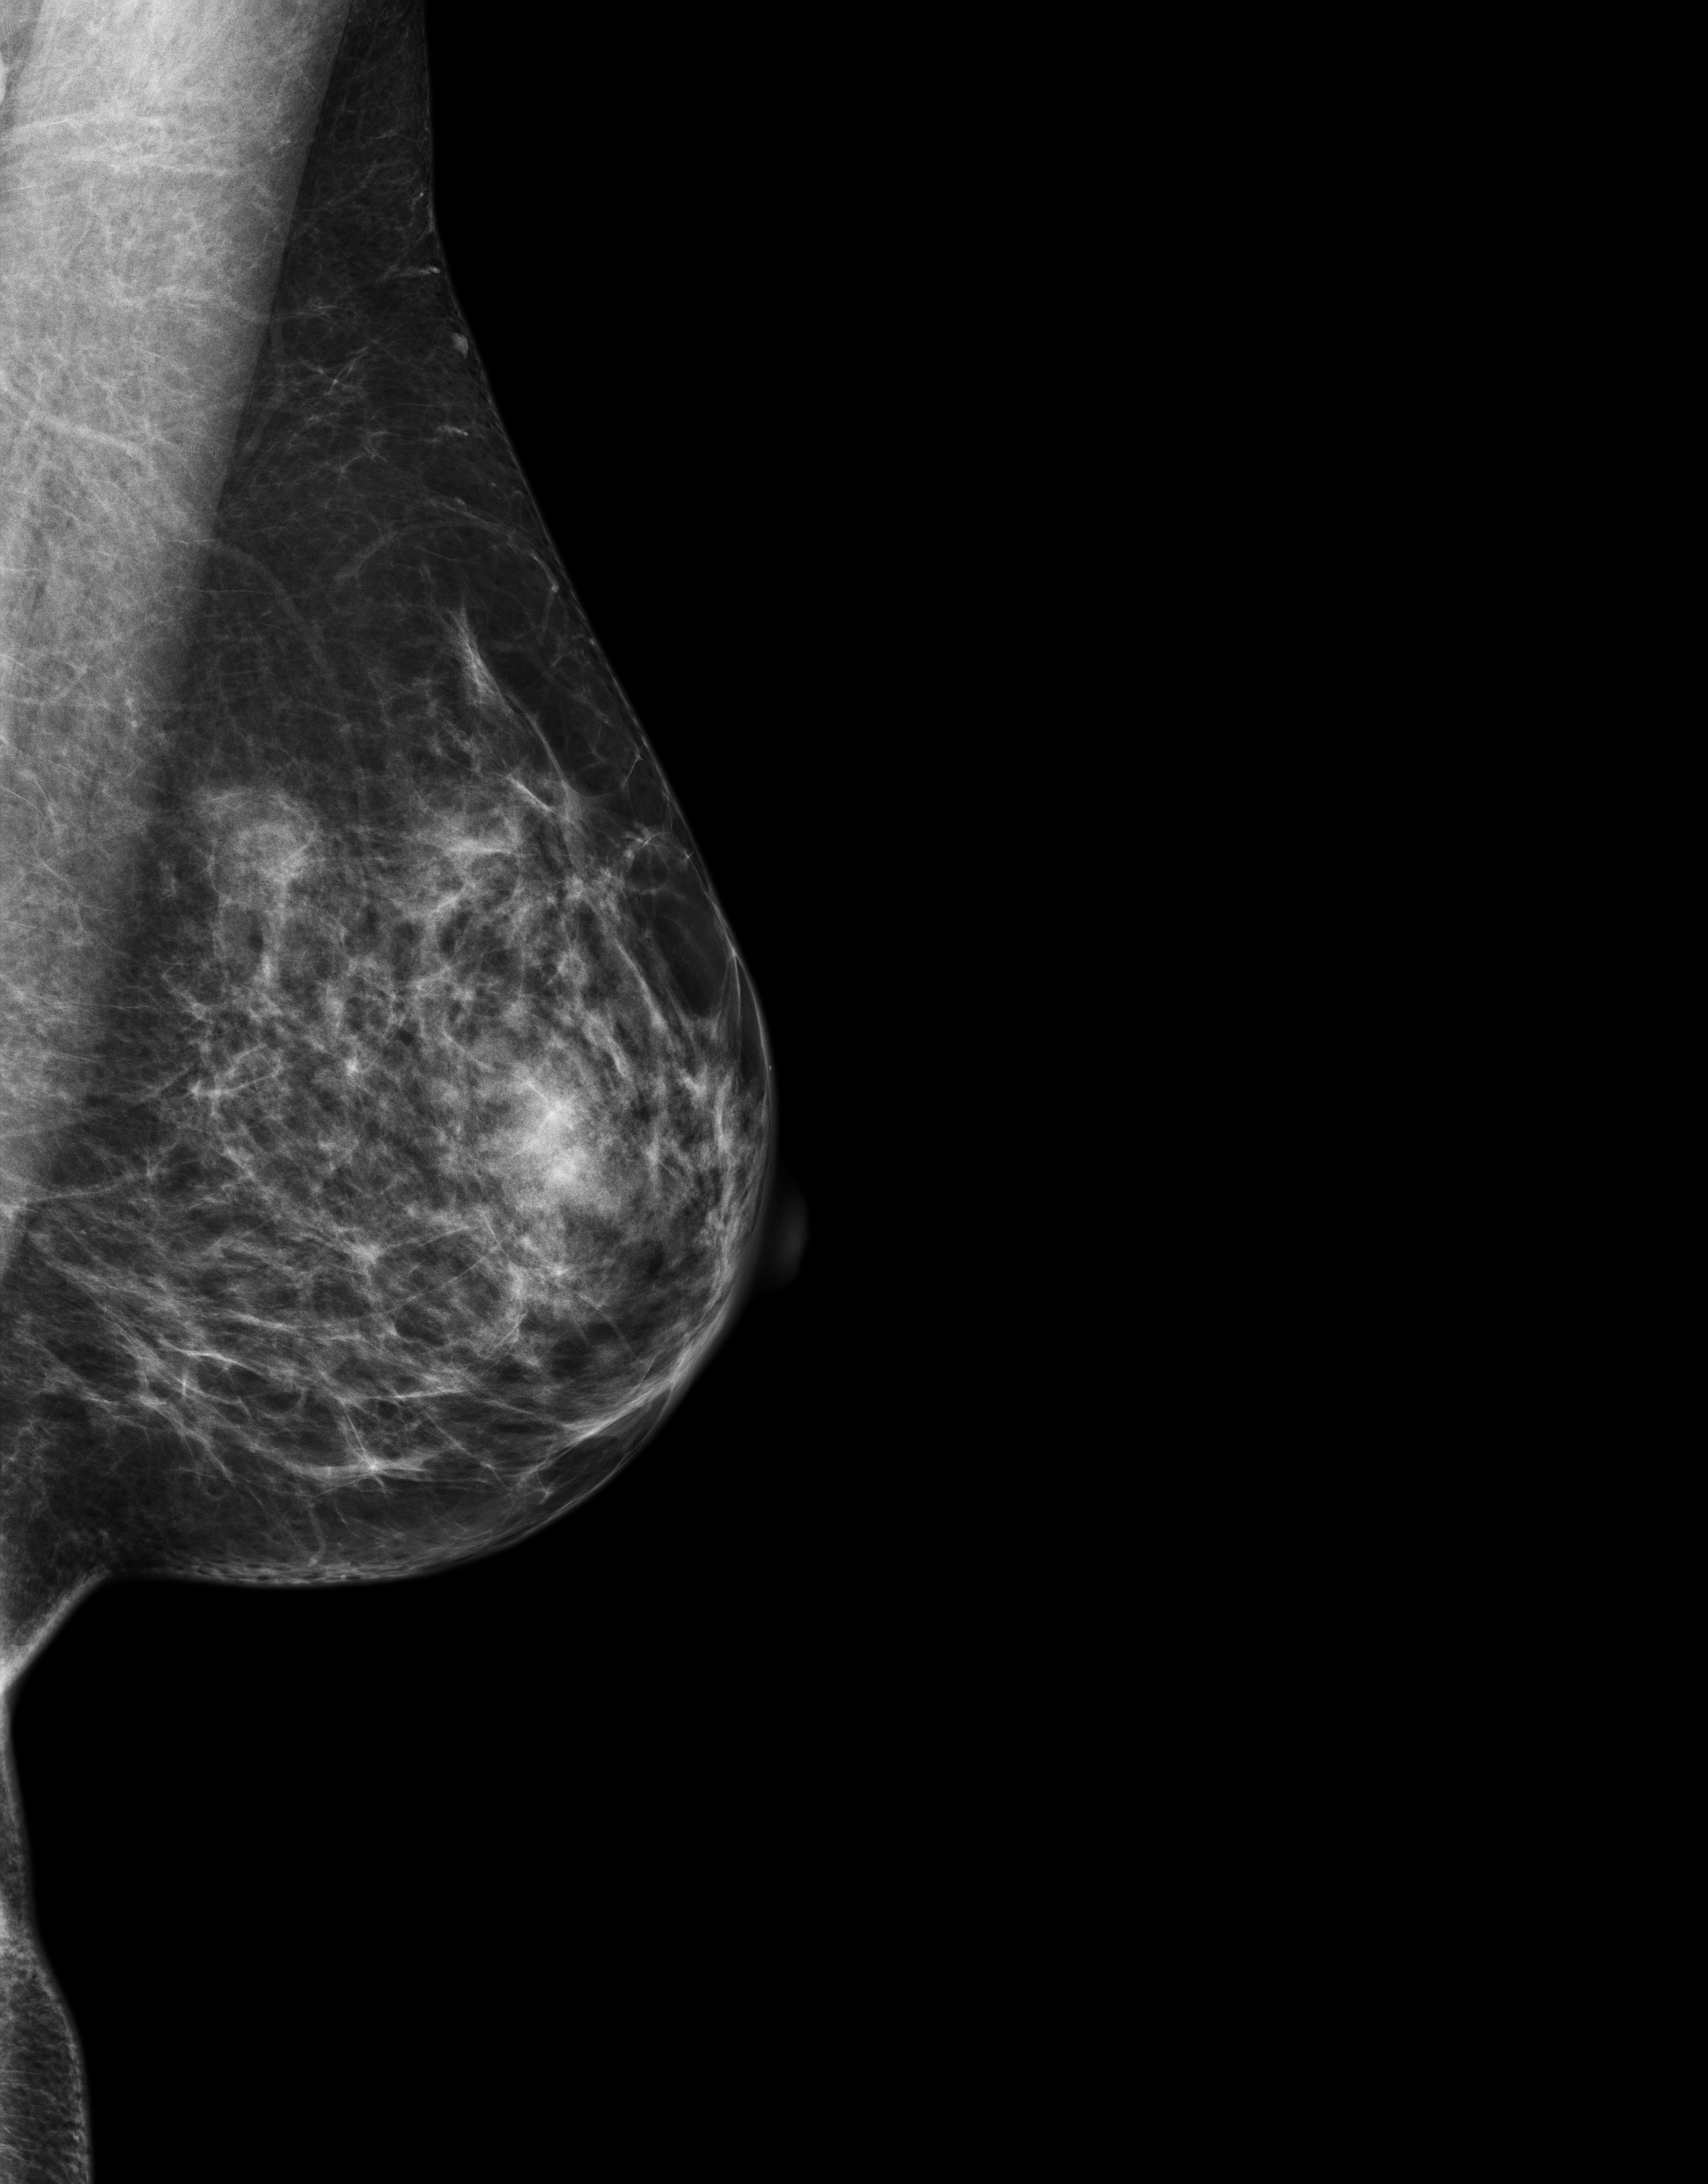
Screening examination, compressed breast thickness 57 mm. Patient aged 56 years (female).
Image type: full-field digital mammogram. Breast: left. Projection: mediolateral oblique (MLO) view. Breast density at the screening exam (both breasts): heterogeneously dense (BI-RADS density category c). Final BI-RADS category for the screening round (tomosynthesis exam, both breasts): category 1. Recall: no recall after this screen.